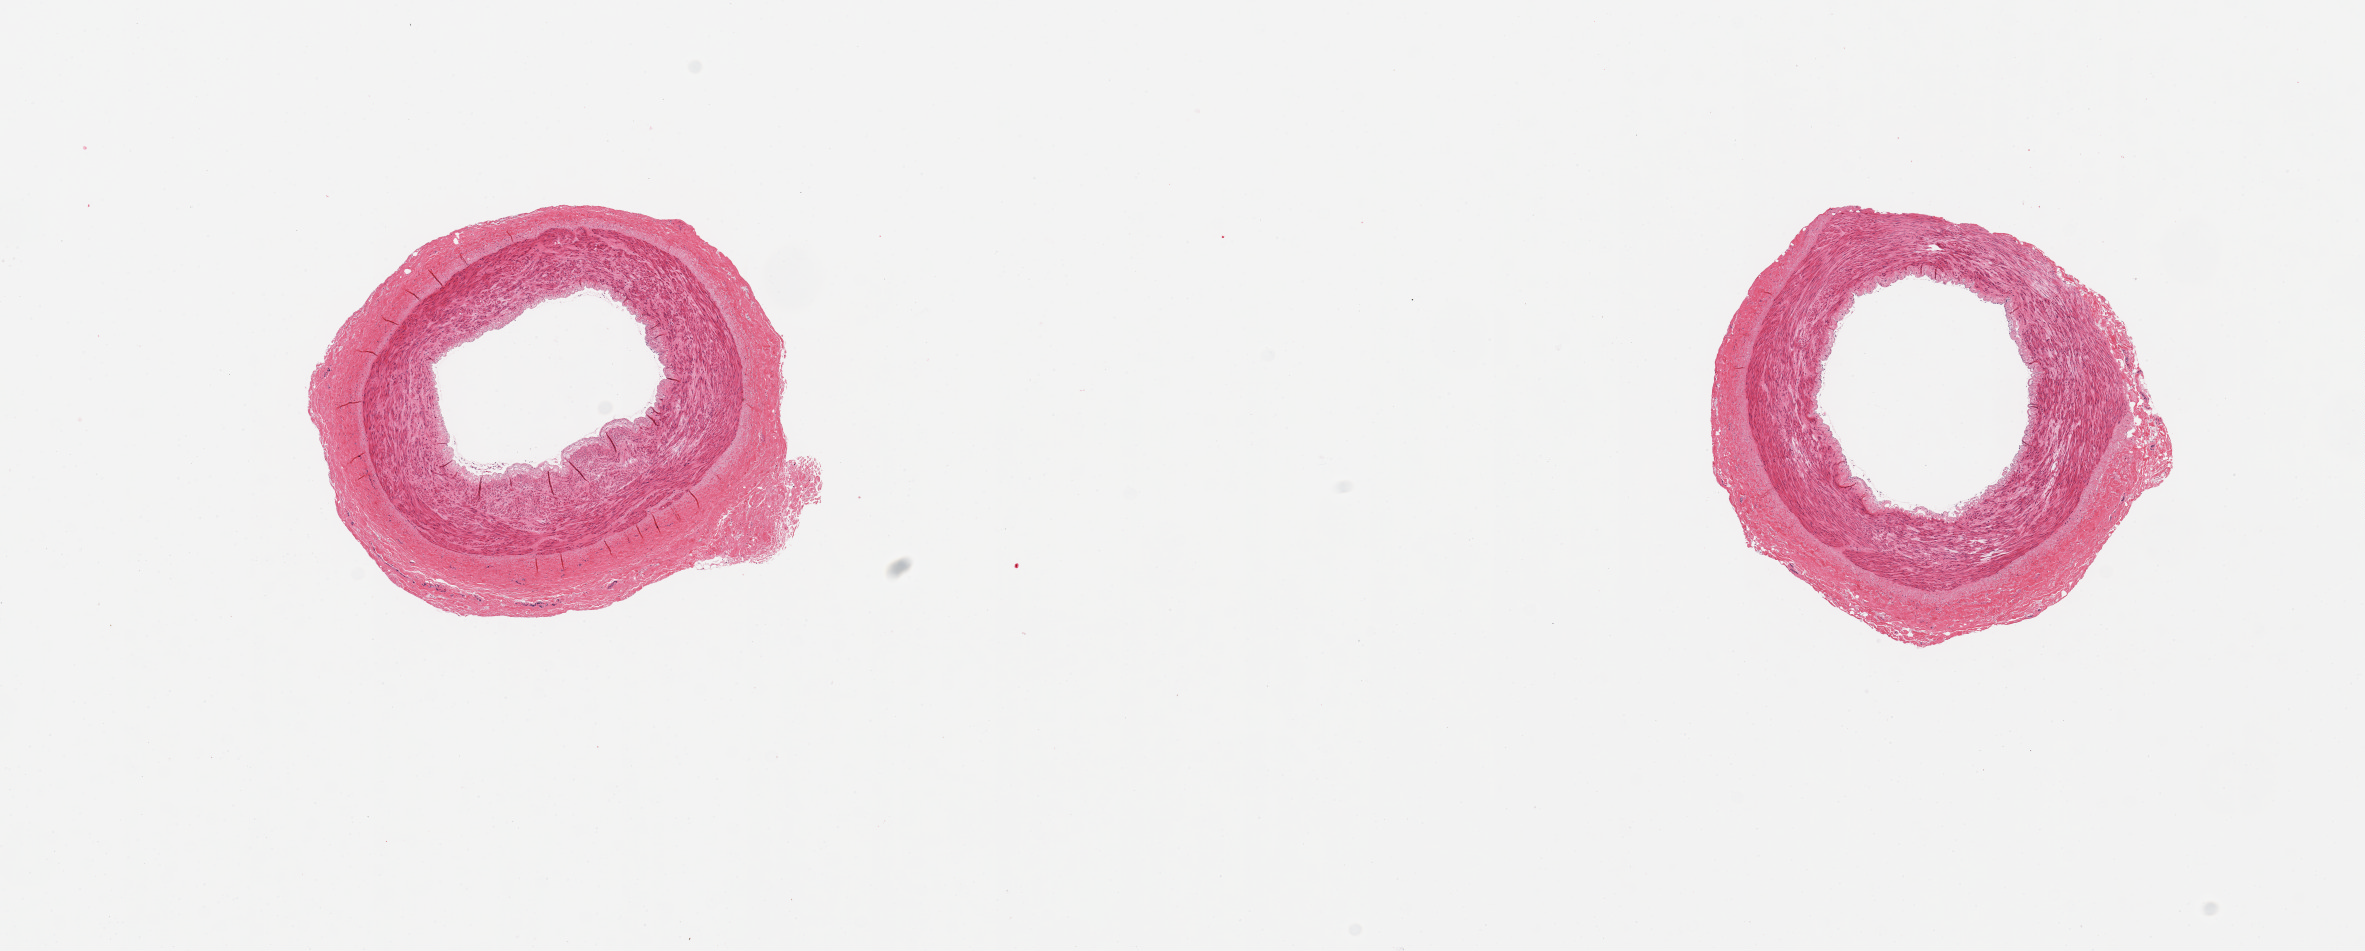
Hematoxylin and eosin (H&E) whole-slide image, brightfield, whole scanned area (about 18.7 x 7.5 mm, from a 20x scan) shown as a low-resolution overview; PAXgene-fixed paraffin-embedded (PFPE) section; sampled site (target tissue): tibial artery; tissue donor sample. Female donor.
* reviewer comment on this tissue sample: 2 pieces, no atherosis, good clean specimen